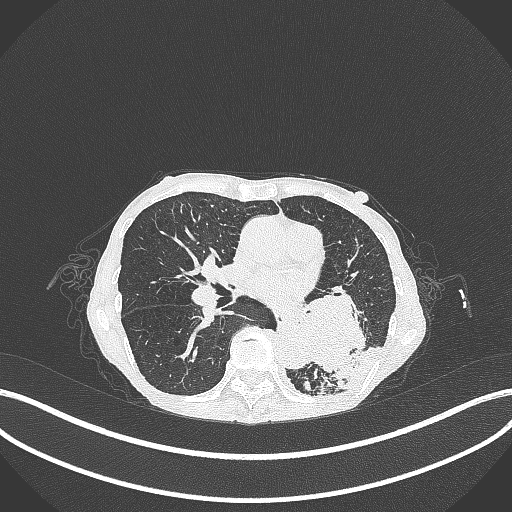
Chest CT, one axial slice. Position 135 of 347 along the scan axis. Reconstruction kernel B70f. Lung window (W 1500 / L -600 HU). 1 mm slice thickness. 512 × 512 image matrix, field of view 400 × 400 mm. Patient: female, 70 years. From the clinical record (not read from this slice): clinical TNM (as recorded): T3 N0 M0; histopathological grade: G3.
Annotated regions visible in this slice (rectangle marked by the reading radiologist):
- lung tumour (recorded histology: small cell carcinoma): box from (x=296, y=278) to (x=377, y=386) px